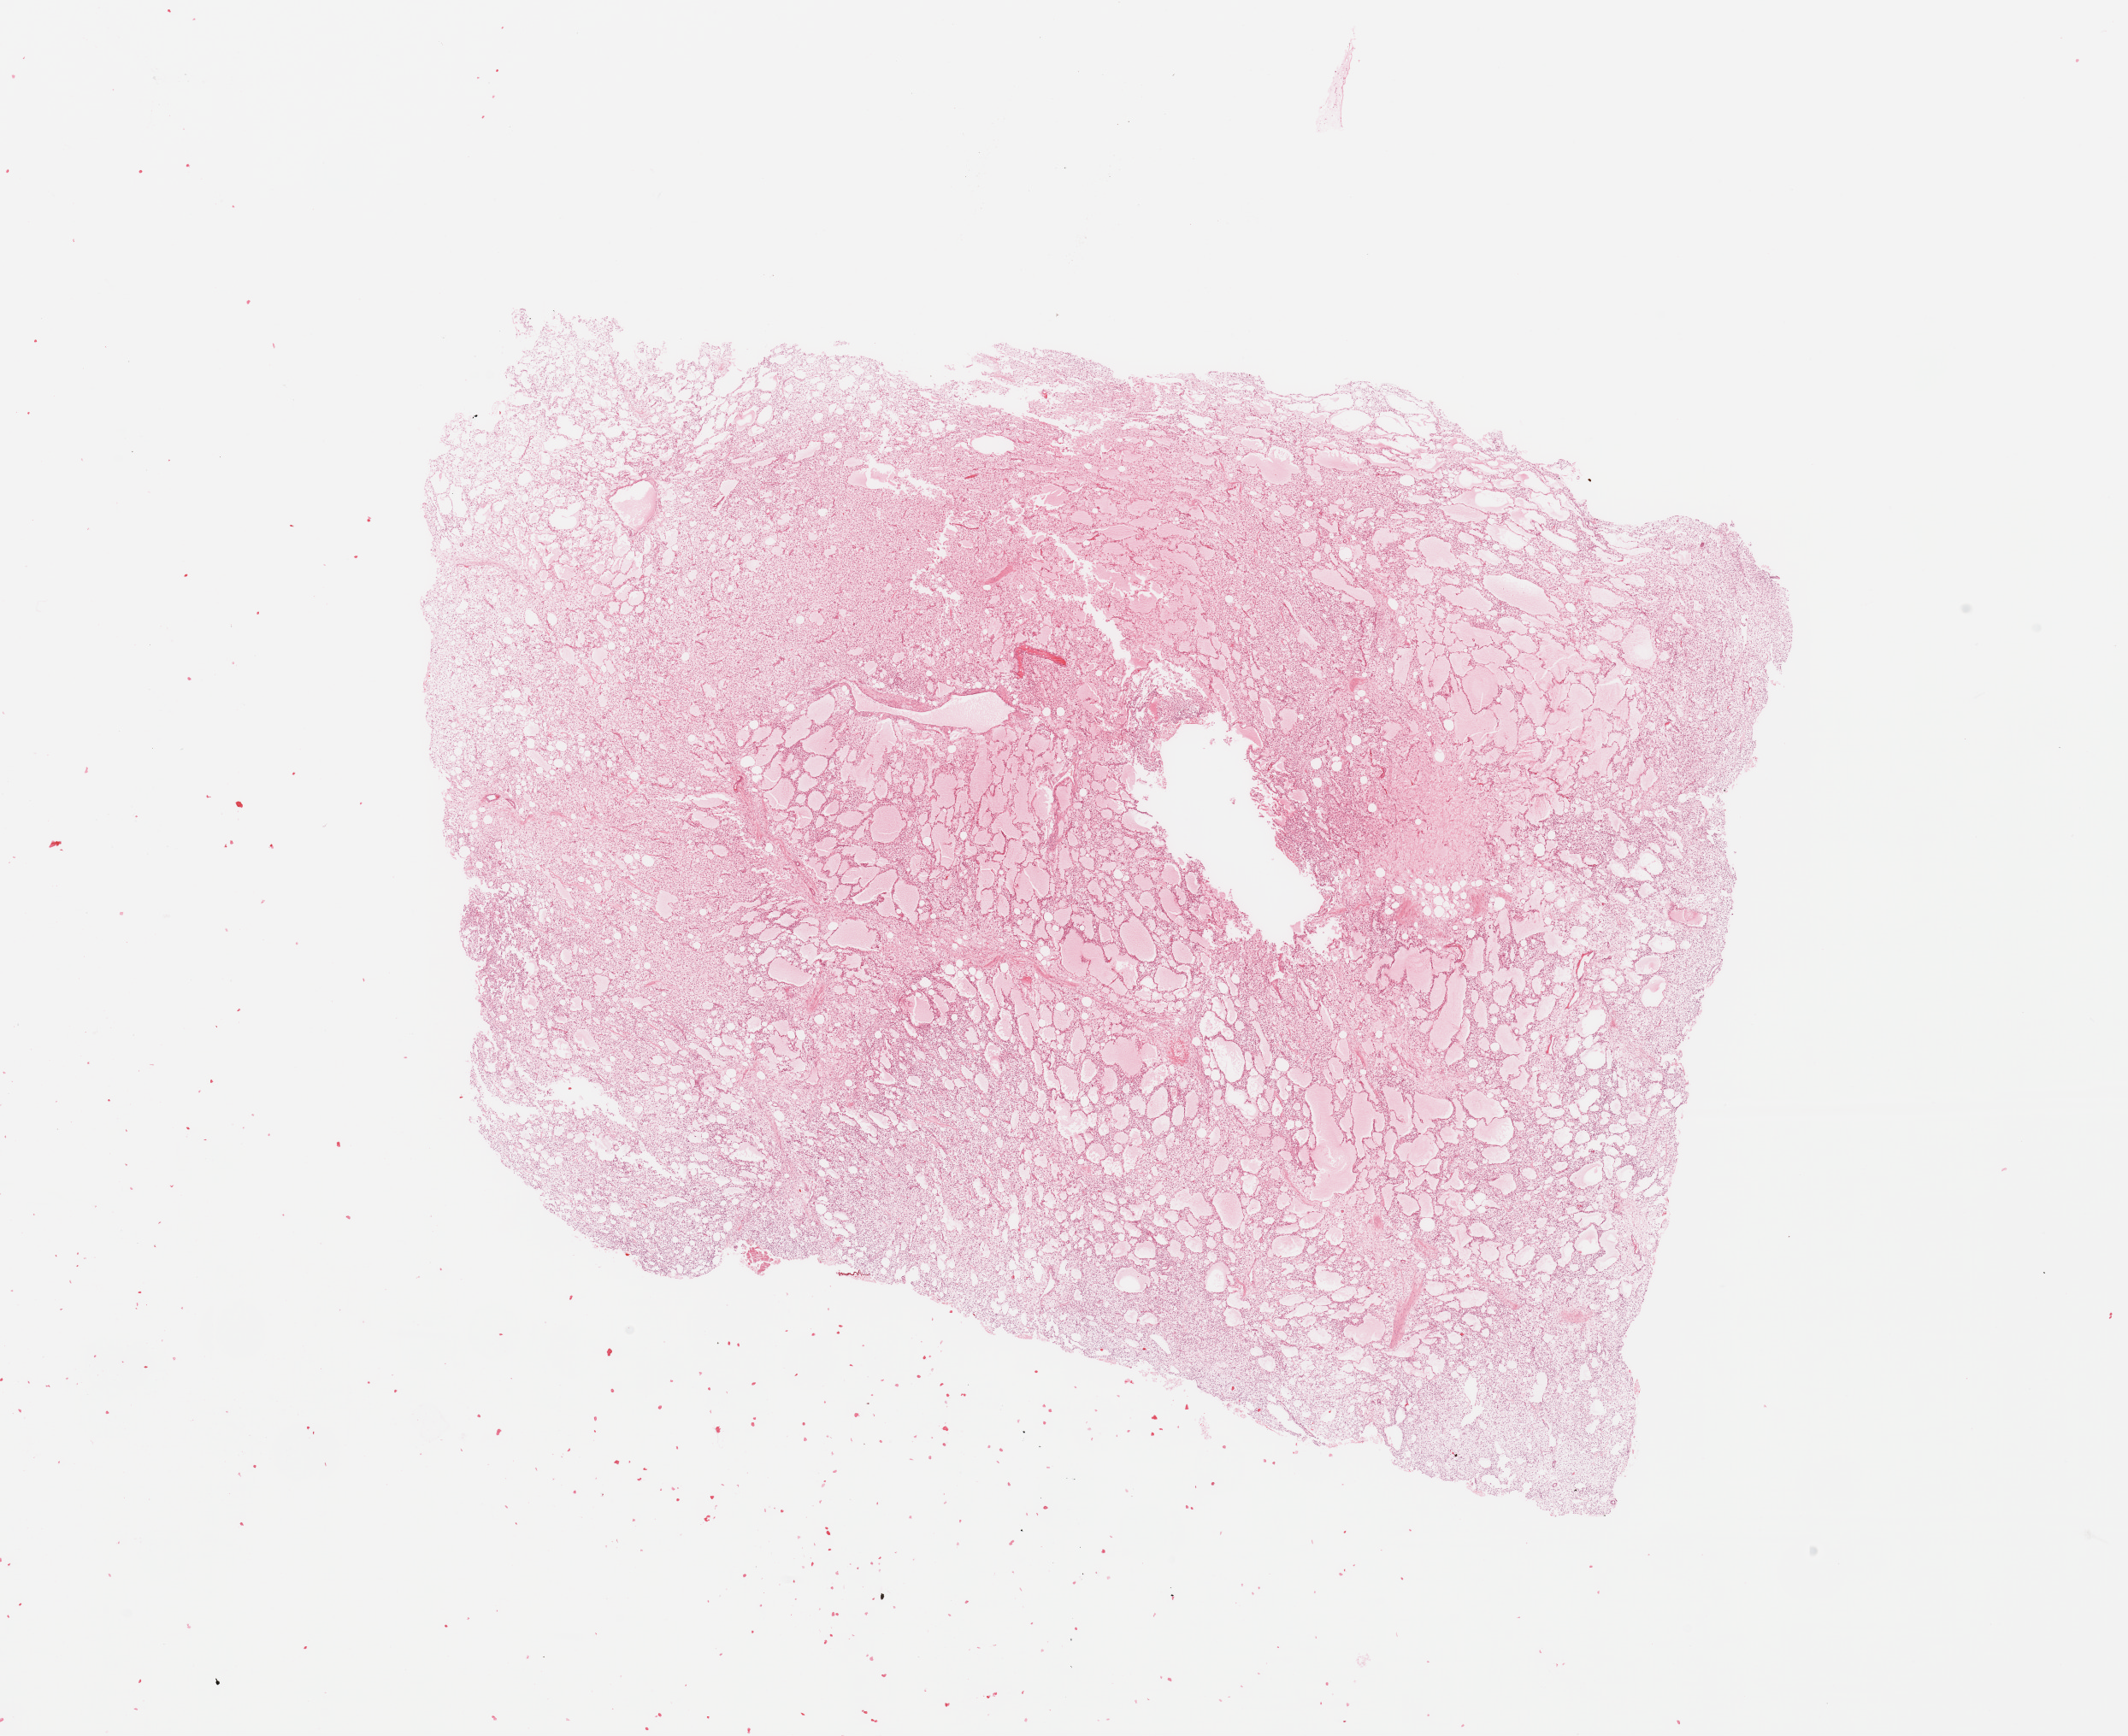
Hematoxylin and eosin (H&E) stained whole-slide image — whole scanned area (about 19.7 x 16.1 mm) shown as a low-resolution overview, tumour tissue sample. Female, 32 y/o.
• primary tumour site (as recorded): lower extremity
• patient diagnosis (cohort enrolment): sarcoma (site not recorded at cohort level)